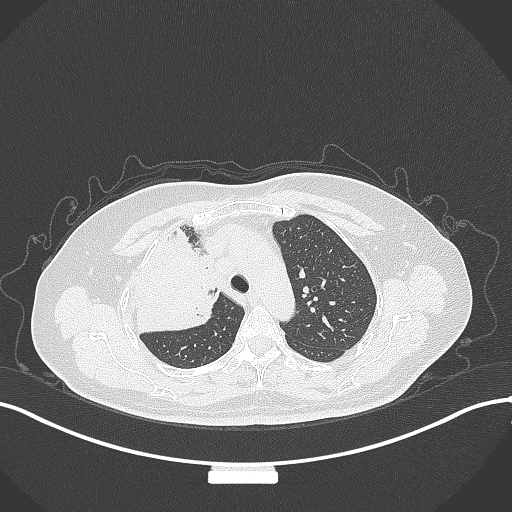
Chest CT, one axial slice. Position 231 of 309 along the scan axis. Lung window (W 1500 / L -600 HU). 1 mm slice thickness. 512 × 512 image matrix. Patient: female, 60 years. From the clinical record (not read from this slice): clinical TNM (as recorded): T3 N1 M1.
Annotated regions visible in this slice (rectangle marked by the reading radiologist):
- lung tumour (recorded histology: adenocarcinoma): bounding box (x1, y1, x2, y2) in pixels: (125, 232, 218, 341)